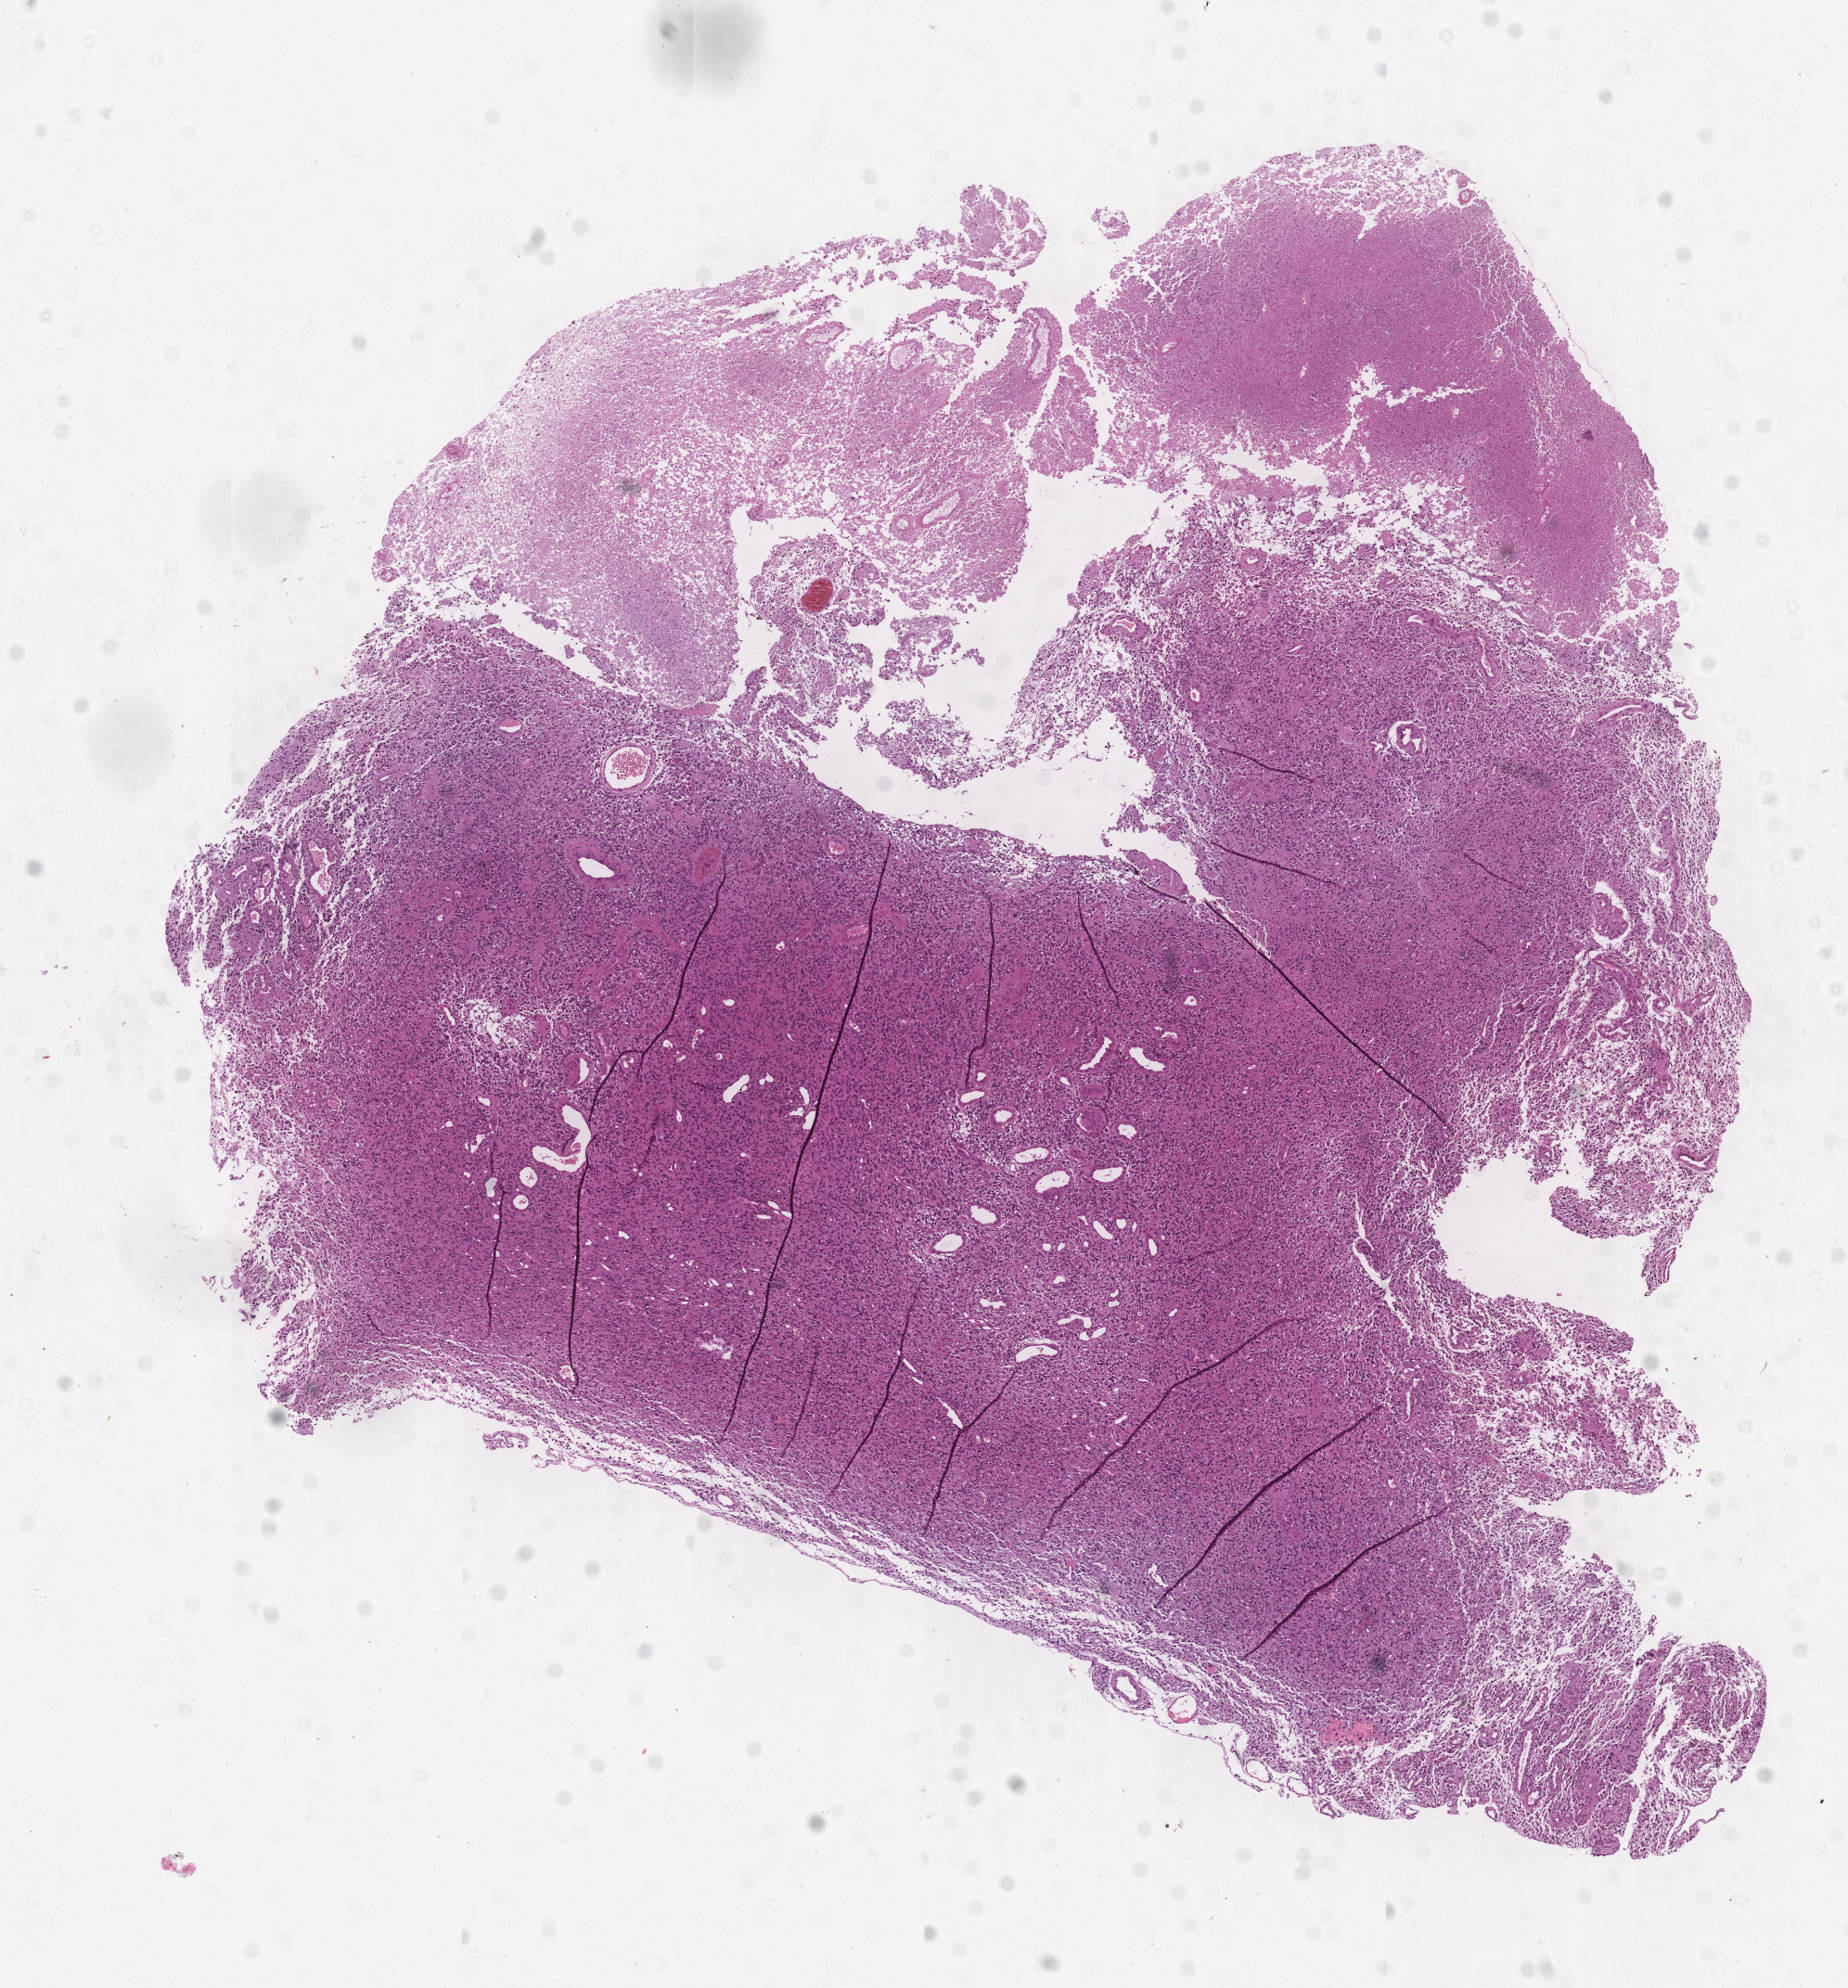
Digitized H&E tissue section (whole slide) — shown as a low-resolution overview of the whole scanned area (about 8.0 x 8.6 mm, acquisition: 20x scan). Tumour tissue sample, sampled site: brain. 62-year-old male patient. Slide review estimates, as recorded: tumour nuclei 70%, necrosis 20%.
* diagnosis: Glioblastoma